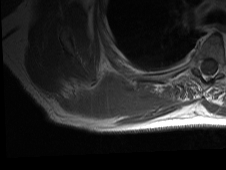
MRI of an extremity soft-tissue mass, one axial slice; slice 22 of 81 in the series (ordered by position); MR volume resampled by the dataset authors to the PET/CT grid (not the native acquisition matrix); 226 × 170 image matrix. Male patient. Case-level facts recorded for this patient, not image findings: histological type: pleiomorphic spindle cell undifferentiated; grade: high; site of the primary tumour: right parascapusular.
Annotated regions visible in this slice (expert contour drawn on MRI and transferred to this co-registered scan by the dataset authors):
- gross tumour volume including surrounding oedema: bounding box <53,75,180,126> (left, top, right, bottom; pixels)
- gross tumour volume (mass): <78,79,129,116>